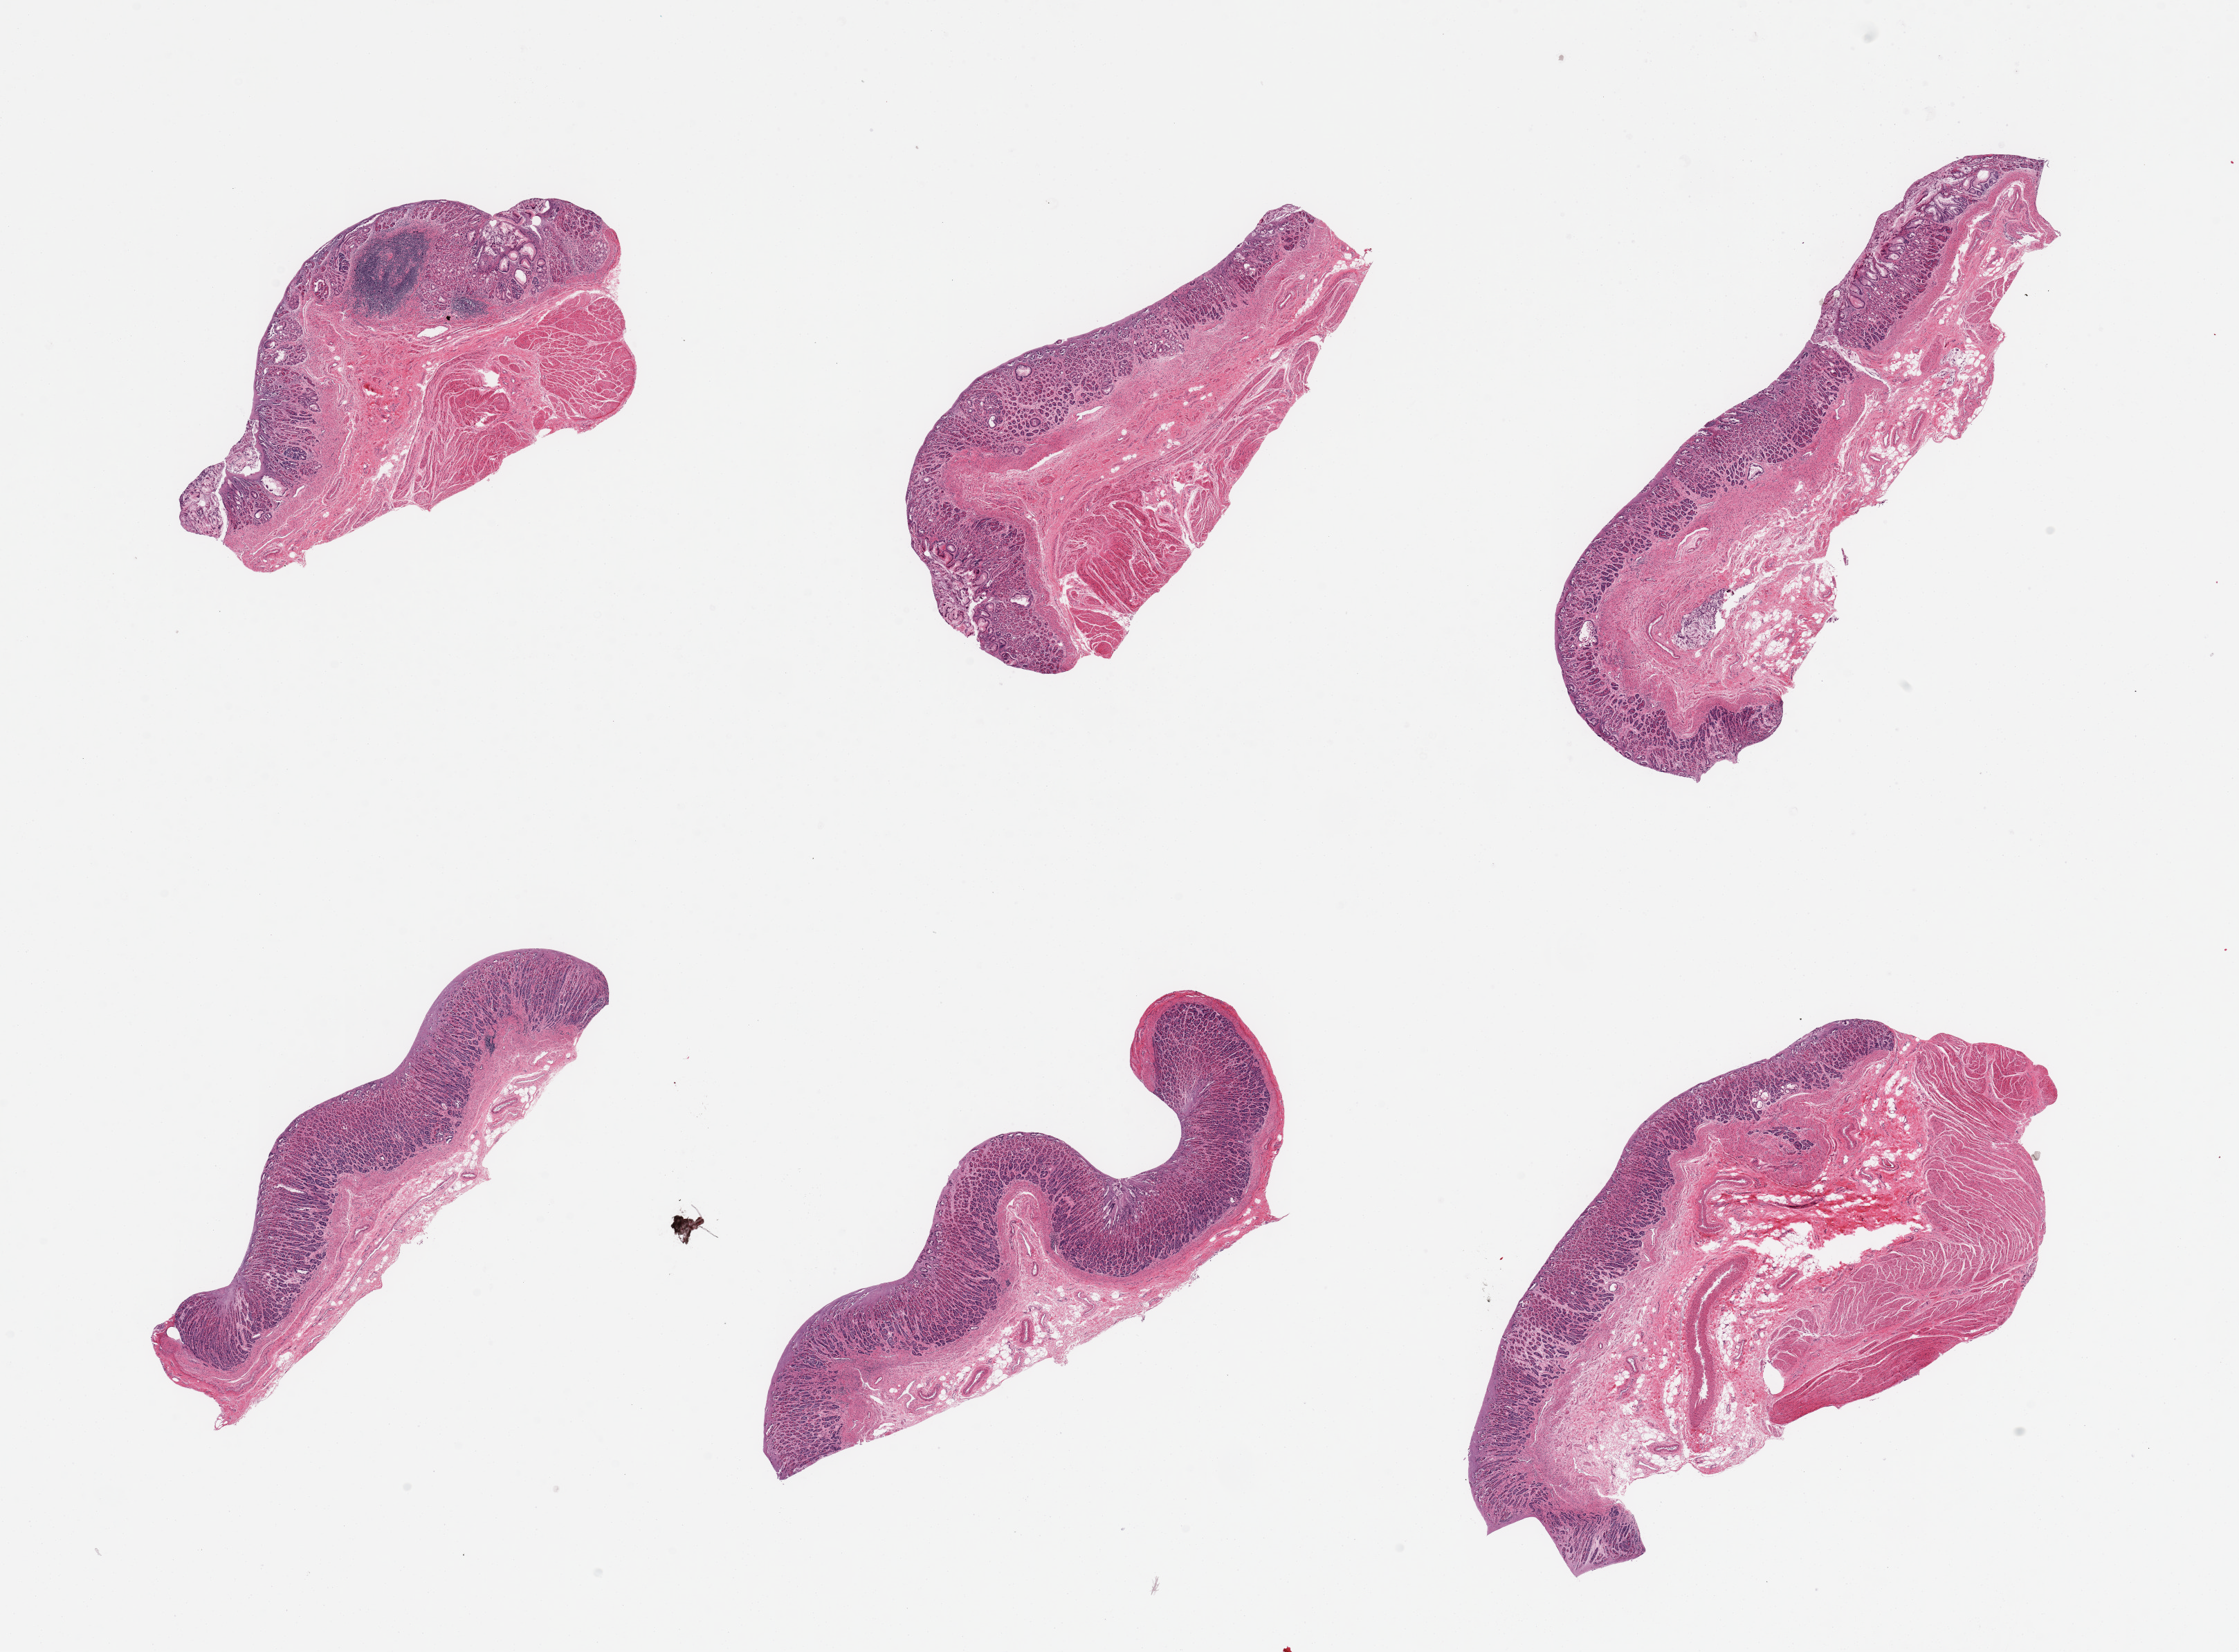
Digitized H&E-stained section — whole scanned area (about 25.6 x 18.9 mm, acquisition: 20x scan) shown as a low-resolution overview. PAXgene-fixed, paraffin-embedded tissue. Section of gastroesophageal junction (target tissue). Tissue donor sample. Donor: male.
* review note (as recorded): 6 pieces; gastric mucosa; 3 pieces contain target muscularis